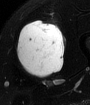
MRI of an extremity soft-tissue mass, one axial slice; position 34 of 65 along the scan axis; T2-weighted fat-saturated; MR volume resampled by the dataset authors to the PET/CT grid (not the native acquisition matrix); 3.27 mm slice thickness; 90 × 105 image matrix, field of view 88 × 103 mm. Male patient. From the clinical record (not read from this slice): histological type: mixoid liposarcoma; grade: low; site of the primary tumour: left thigh.
Outlined on this slice (expert contour drawn on MRI and transferred to this co-registered scan by the dataset authors):
- gross tumour volume (mass): bounding box [x1, y1, x2, y2] px = [16, 21, 65, 79]